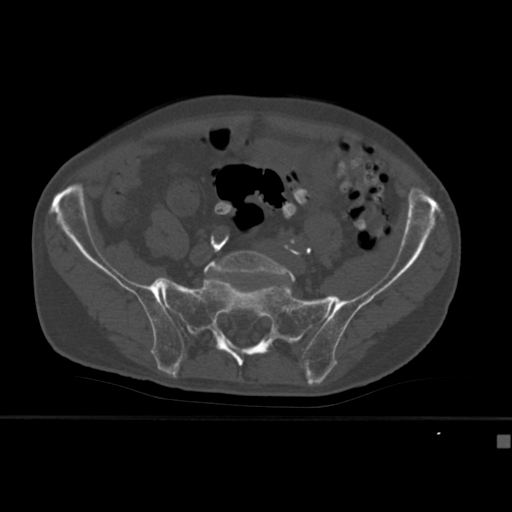
CT including the spine, one axial slice. Position 71 of 430 along the scan axis. Bone window (W 1800 / L 400 HU). 512 × 512 image matrix, field of view 337 × 337 mm. Male patient, age 64 years. Case-level facts recorded for this patient, not image findings: primary cancer: uterus.
Structures marked on this image (semi-automatically segmented with operator editing):
- L5 vertebra: bounding box (x1, y1, x2, y2) in pixels: (204, 251, 296, 283)